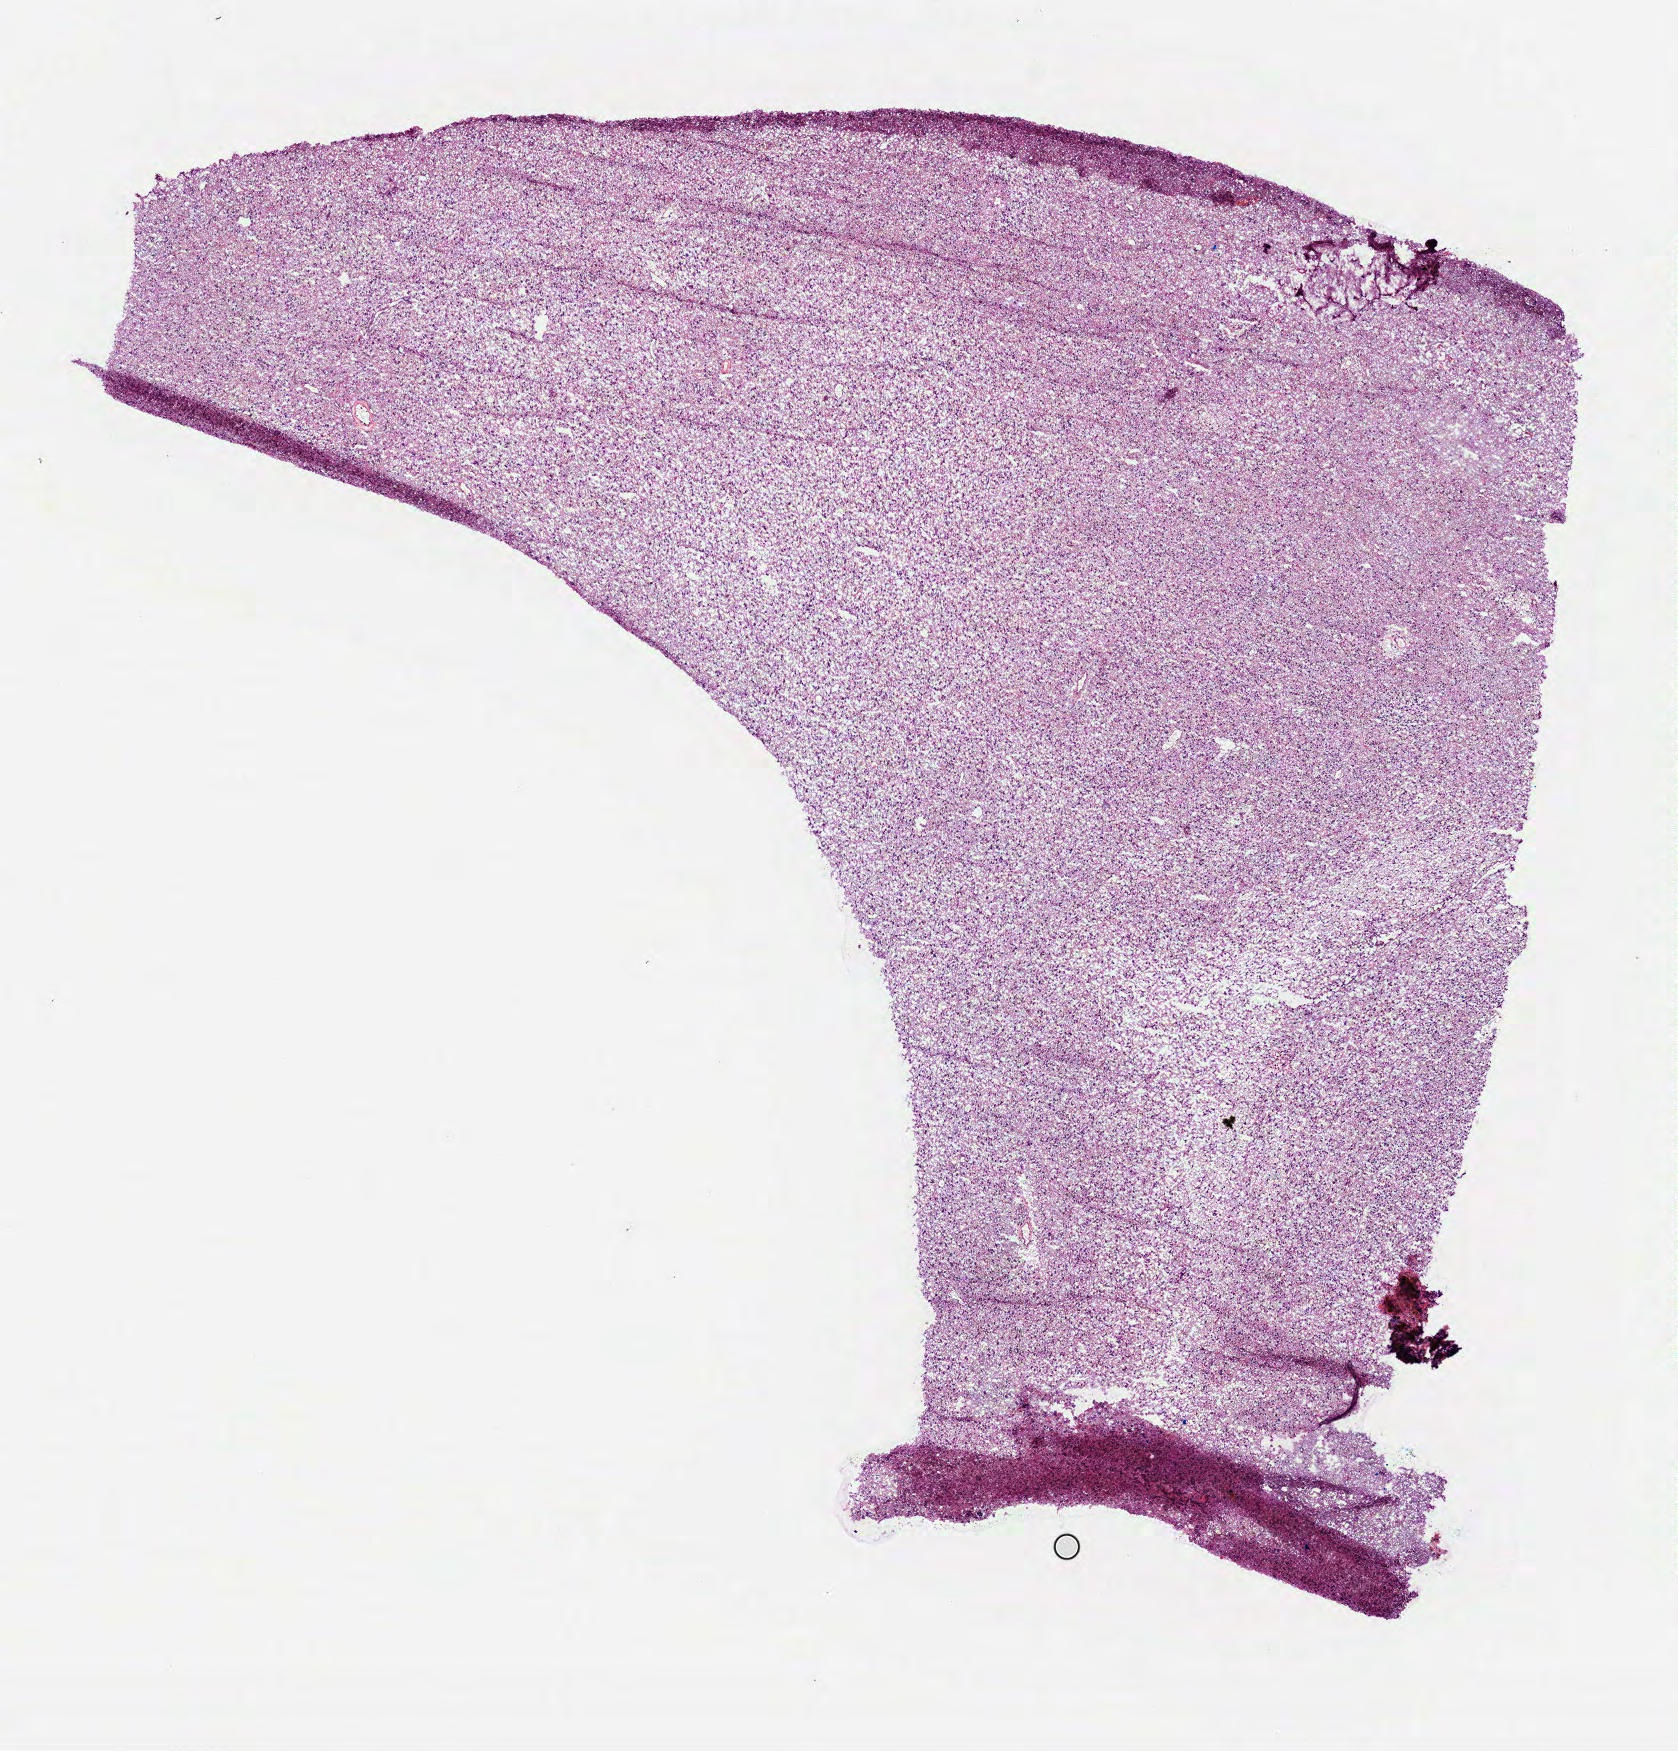
Digitized Hematoxylin and eosin (H&E) stained tissue section (whole slide) — whole scanned area (about 6.8 x 7.1 mm) shown as a low-resolution overview. Frozen section. Sample: primary tumour, brain. Female patient; age at initial diagnosis 45 years.
Histologic diagnosis: Astrocytoma, anaplastic (cerebrum).